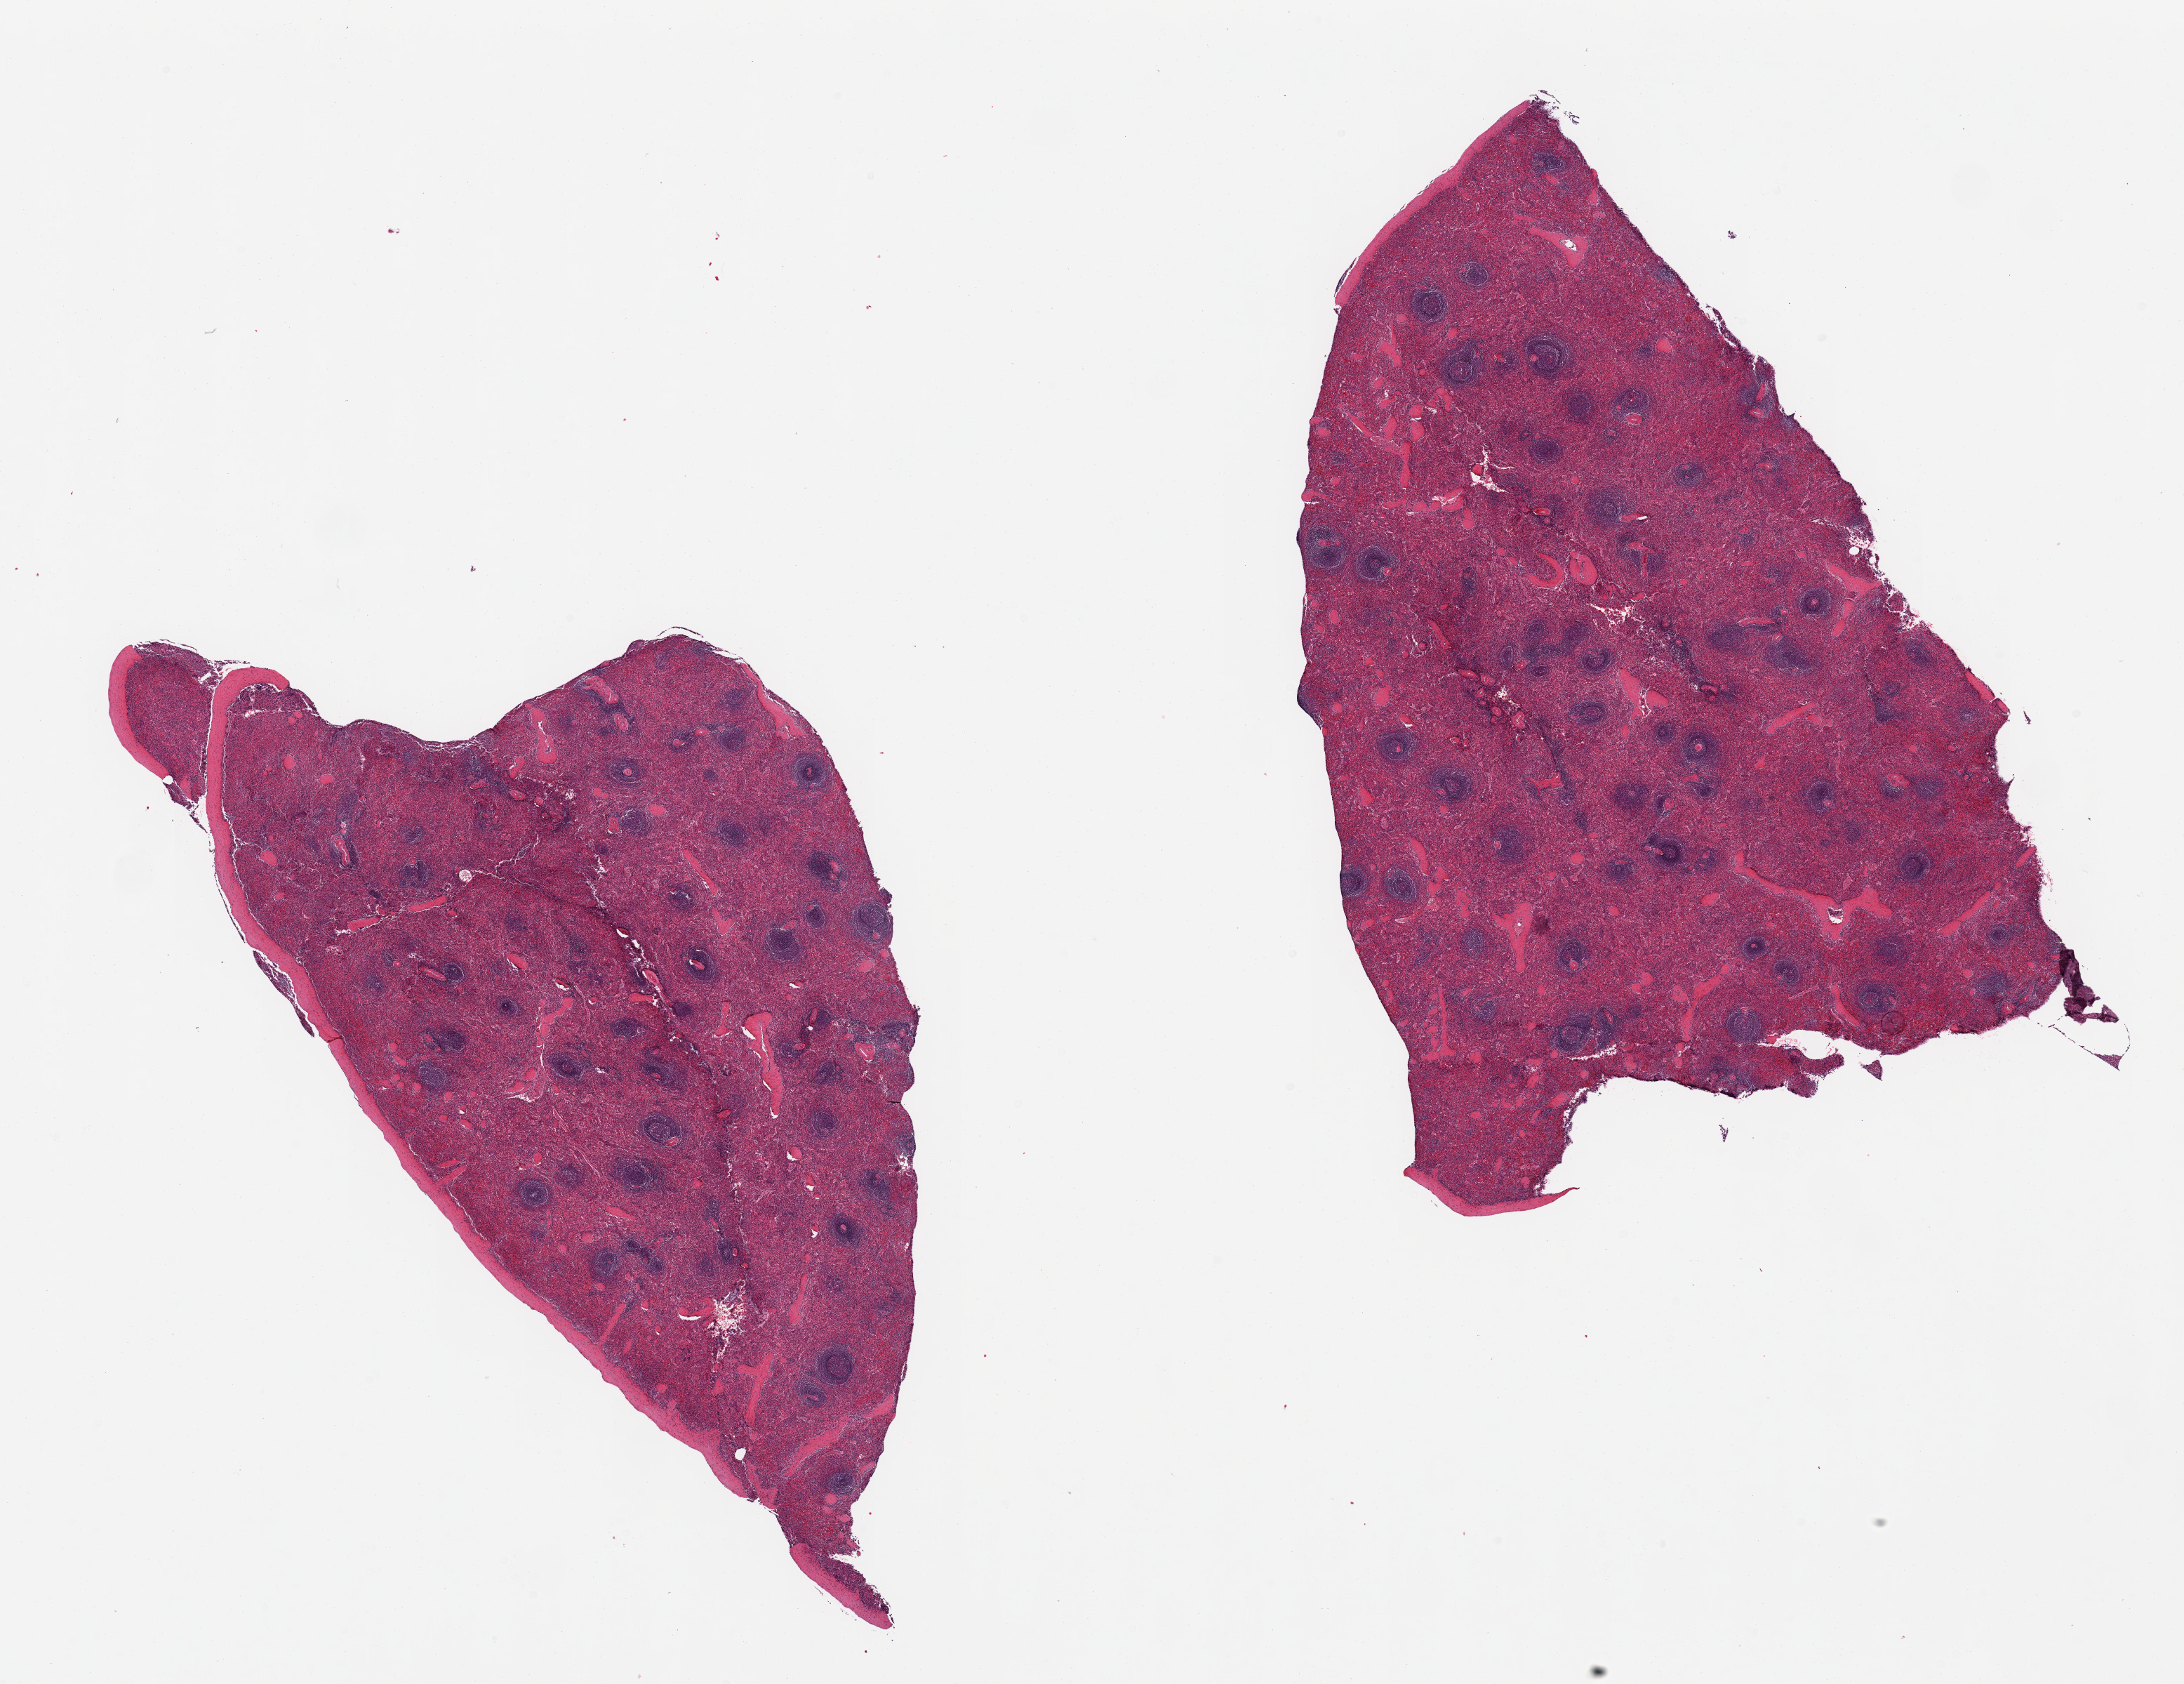
Digitized hematoxylin and eosin (H&E)-stained section — low-resolution overview of the scanned area, about 24.6 x 19.0 mm. PAXgene-fixed, paraffin-embedded tissue. Section of spleen (target tissue). Tissue donor sample. Donor sex: male.
Review note (as recorded): 2 pieces, no abnormalities.